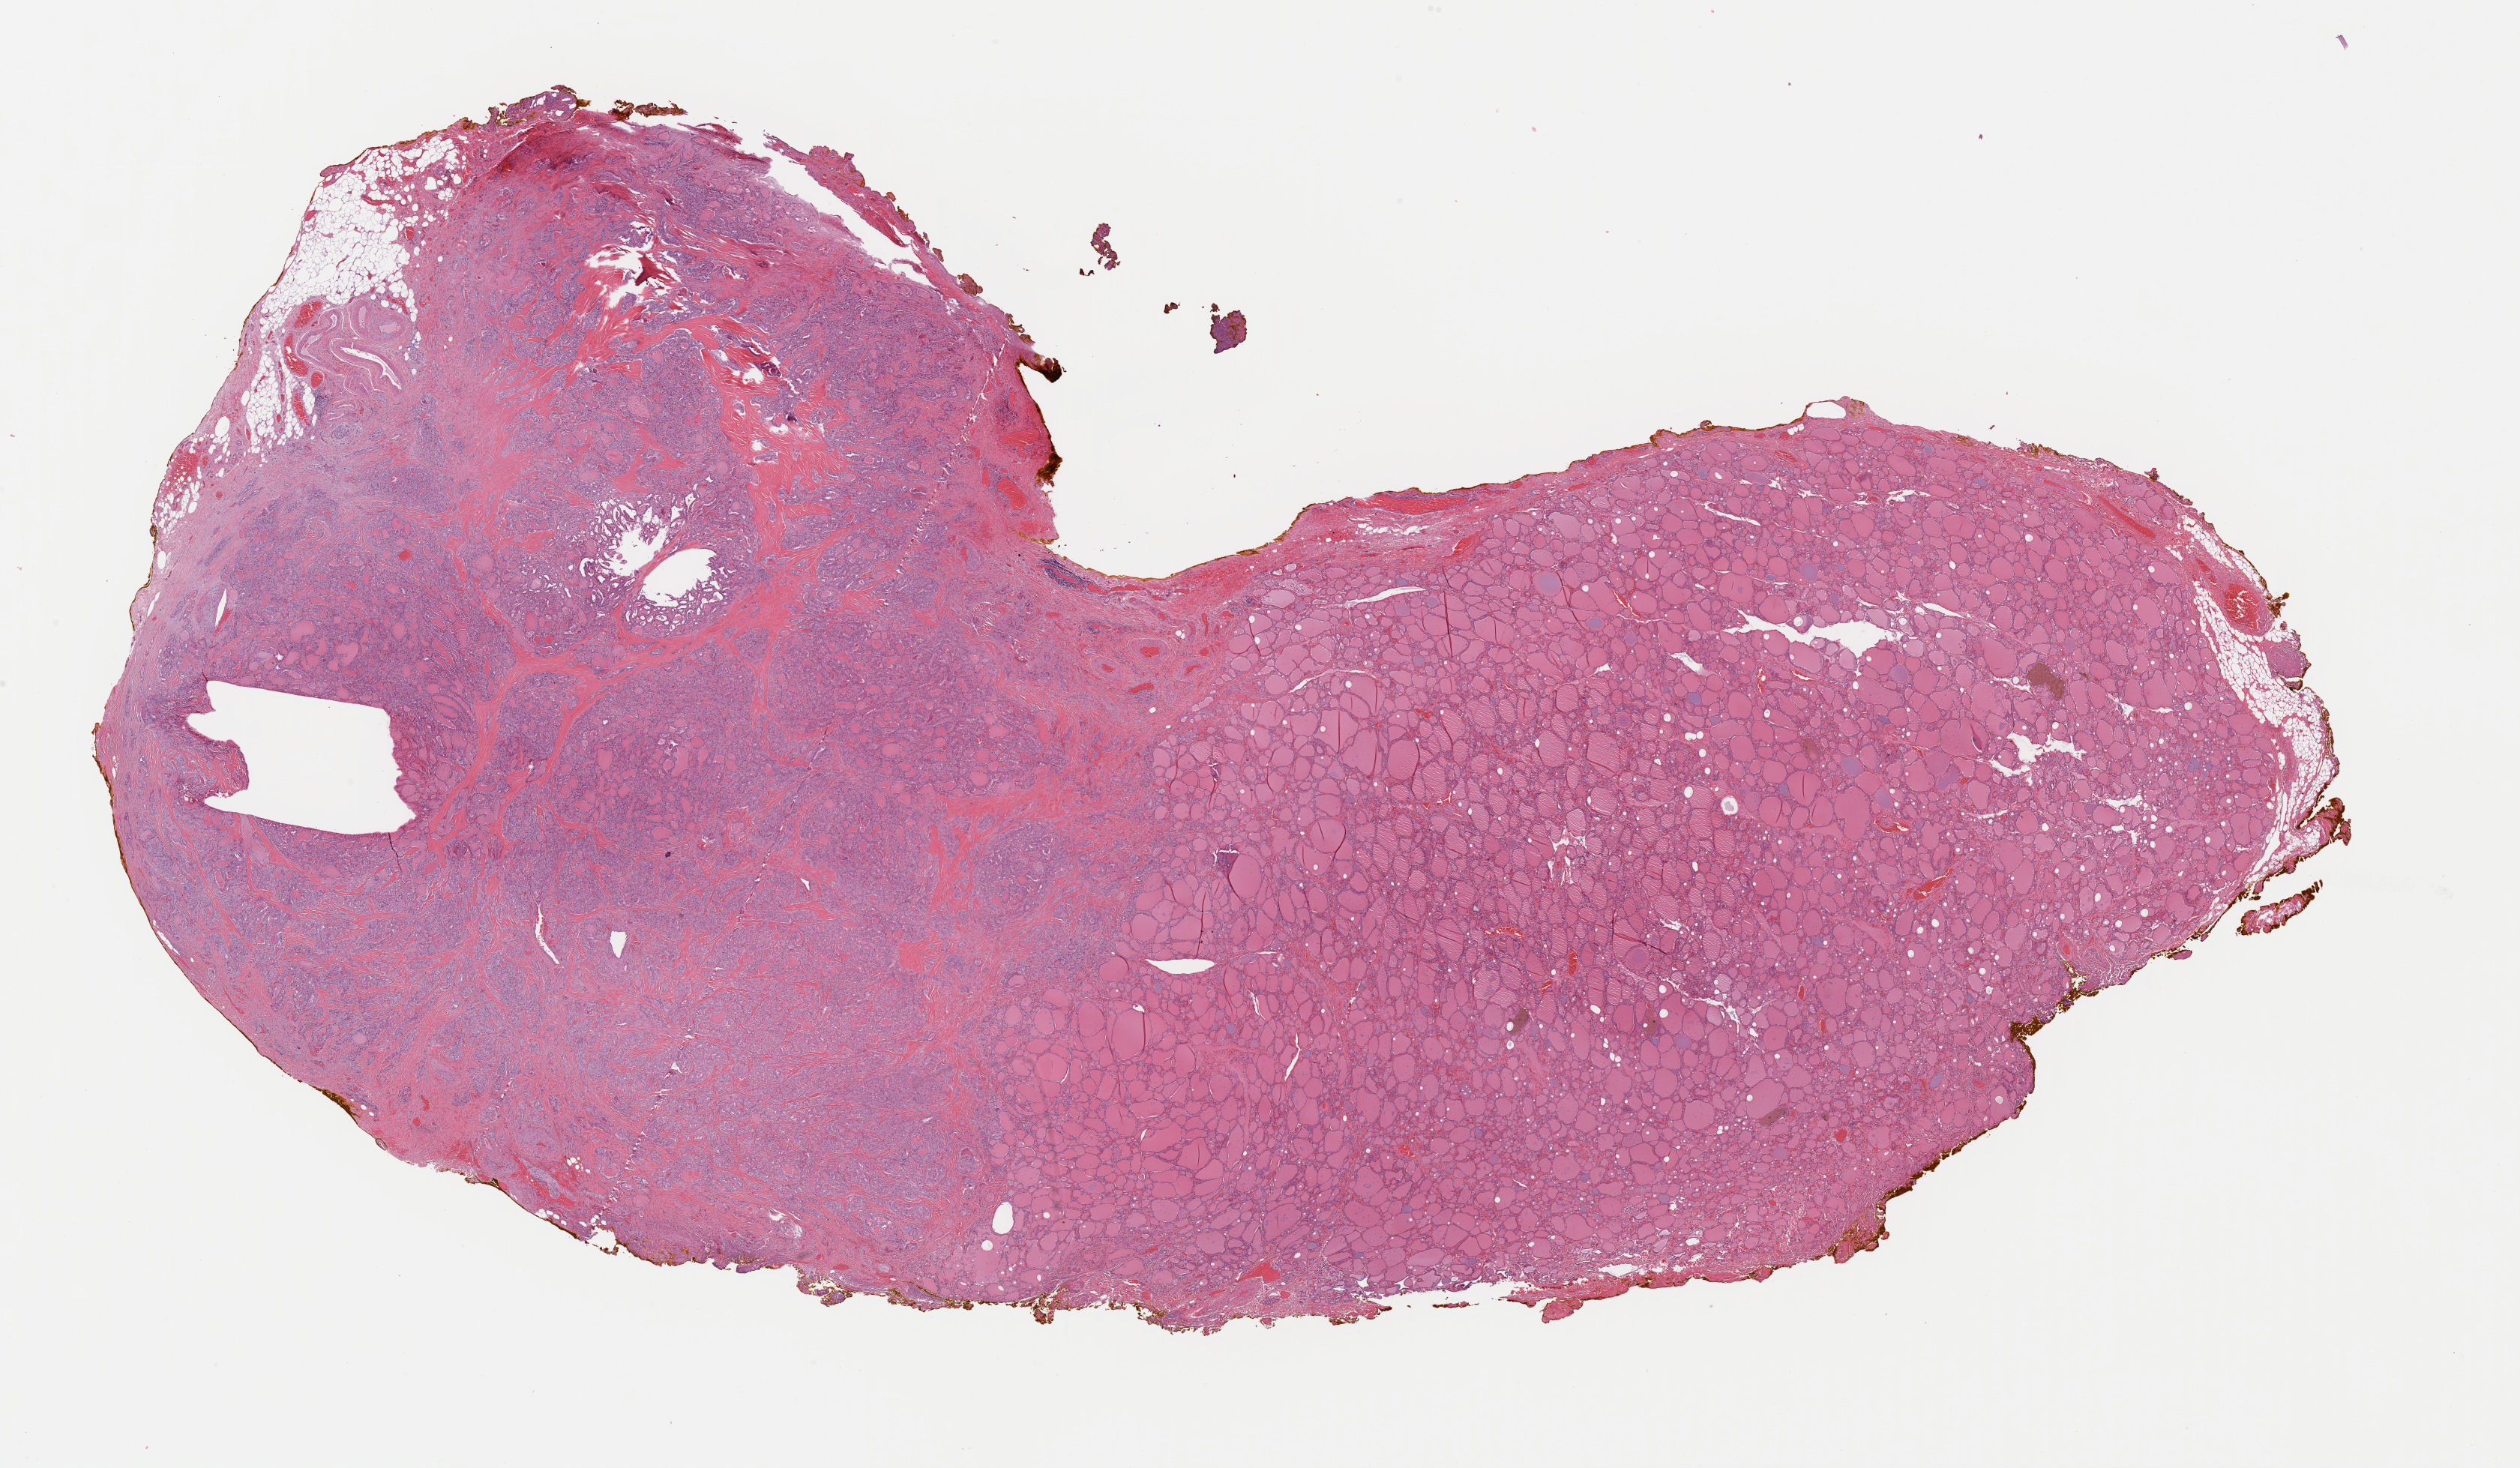
H&E-stained whole-slide image — shown as a low-resolution overview of the whole scanned area (about 26.5 x 15.5 mm), formalin-fixed paraffin-embedded (FFPE) diagnostic section, sample: primary tumour, thyroid. Female, age 46 years at initial diagnosis.
Lymph nodes positive (case pathology): 0 of 5 examined. AJCC pathologic stage: I. Histologic diagnosis: Papillary adenocarcinoma, NOS (thyroid gland). Laterality: midline.